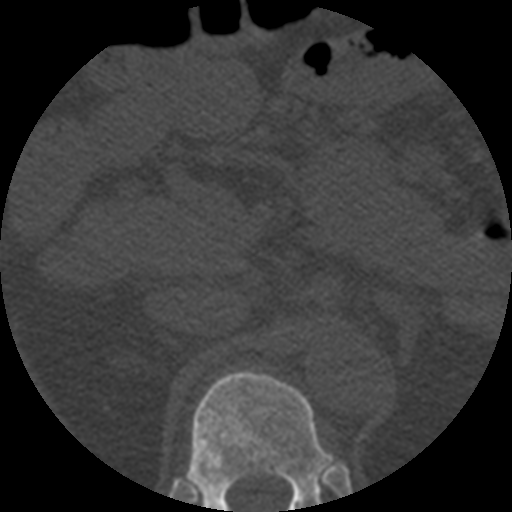
CT including the spine, one axial slice; reconstruction kernel STANDARD; 120 kVp; bone window (W 1800 / L 400 HU); 1.25 mm slice thickness; 512 × 512 image matrix, field of view 160 × 160 mm. Patient age 57 years. From the clinical record (not read from this slice): primary cancer: prostate.
Outlined on this slice (semi-automatic segmentation, software-assisted and operator-edited):
- T12 vertebra: bounding box (x1, y1, x2, y2) in pixels: (186, 370, 334, 512)